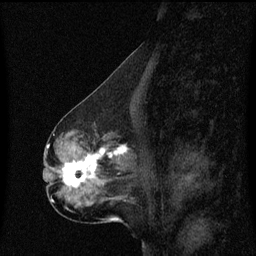
Breast MRI (dynamic contrast-enhanced), one sagittal slice. Slice 28 of 60 in the series (ordered by position). Dynamic contrast-enhanced series, image 2 of 3 at this slice position (ordered by acquisition). 1.5 T. TE 4.2 ms, TR 8.4 ms. 2 mm slice thickness. 256 × 256 image matrix, field of view 200 × 200 mm. Female patient, age 50 years. Case-level facts recorded for this patient, not image findings: setting: breast cancer imaged before/during neoadjuvant chemotherapy; receptor status: HR-positive, HER2-negative.
Structures marked on this image (semi-automatic segmentation, software-assisted and operator-edited):
- analysis volume of interest (the breast-tissue region the enhancement analysis was run in; not a lesion): bounding box [x1, y1, x2, y2] px = [55, 140, 133, 191]
- tumour enhancement mask (voxels above the 70 % enhancement threshold inside the analysis volume of interest): [63, 146, 128, 189]